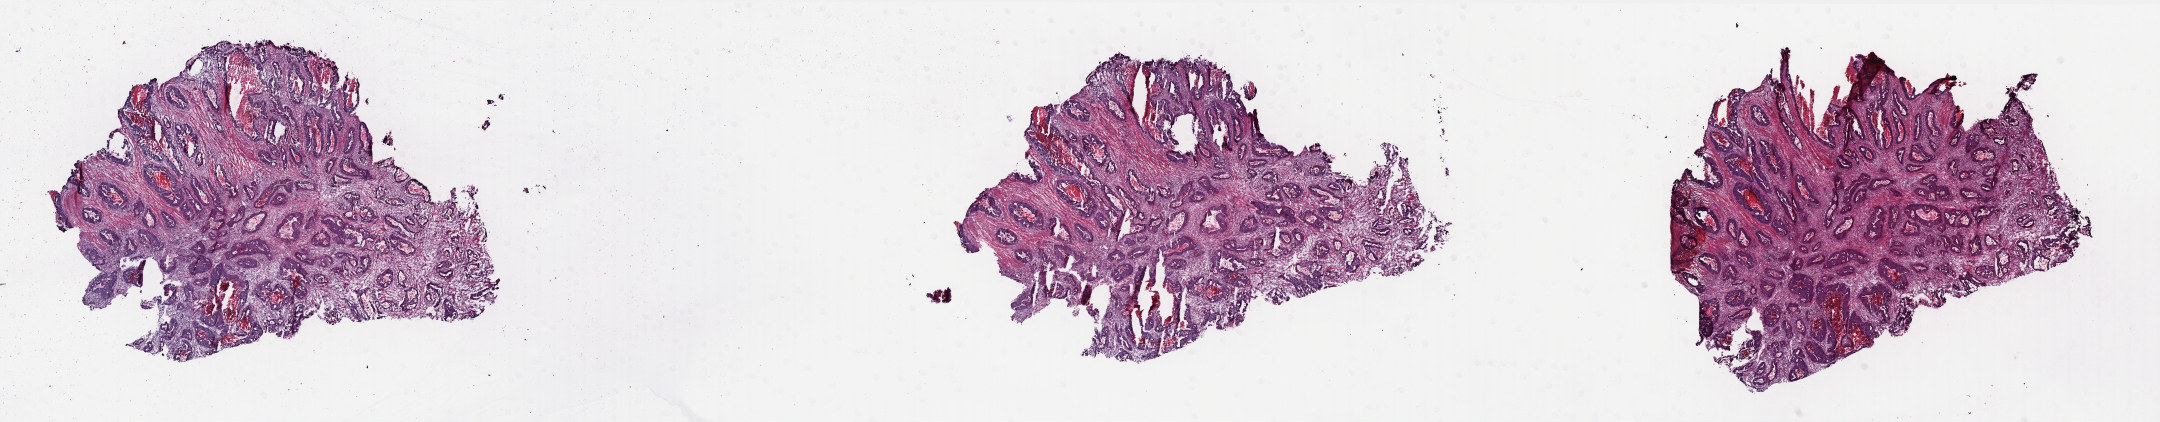
Whole-slide histology image, Hematoxylin and eosin (H&E) stained, shown as a low-resolution overview of the whole scanned area (about 34.6 x 6.8 mm), frozen section from the bottom of the tissue portion, primary tumour sample from the colon. Patient: female, age at initial diagnosis 82 years. Slide review estimates, as recorded: tumour cells 80%, tumour nuclei 60%, normal cells 0%, stromal cells 17%, necrosis 3%. Infiltration values recorded for this section: lymphocyte infiltration 3%, monocyte infiltration 3%, neutrophil infiltration 1%.
TNM: T3 N1 M1. AJCC pathologic stage: IV (6th edition). Histologic diagnosis: Adenocarcinoma, NOS (cecum).